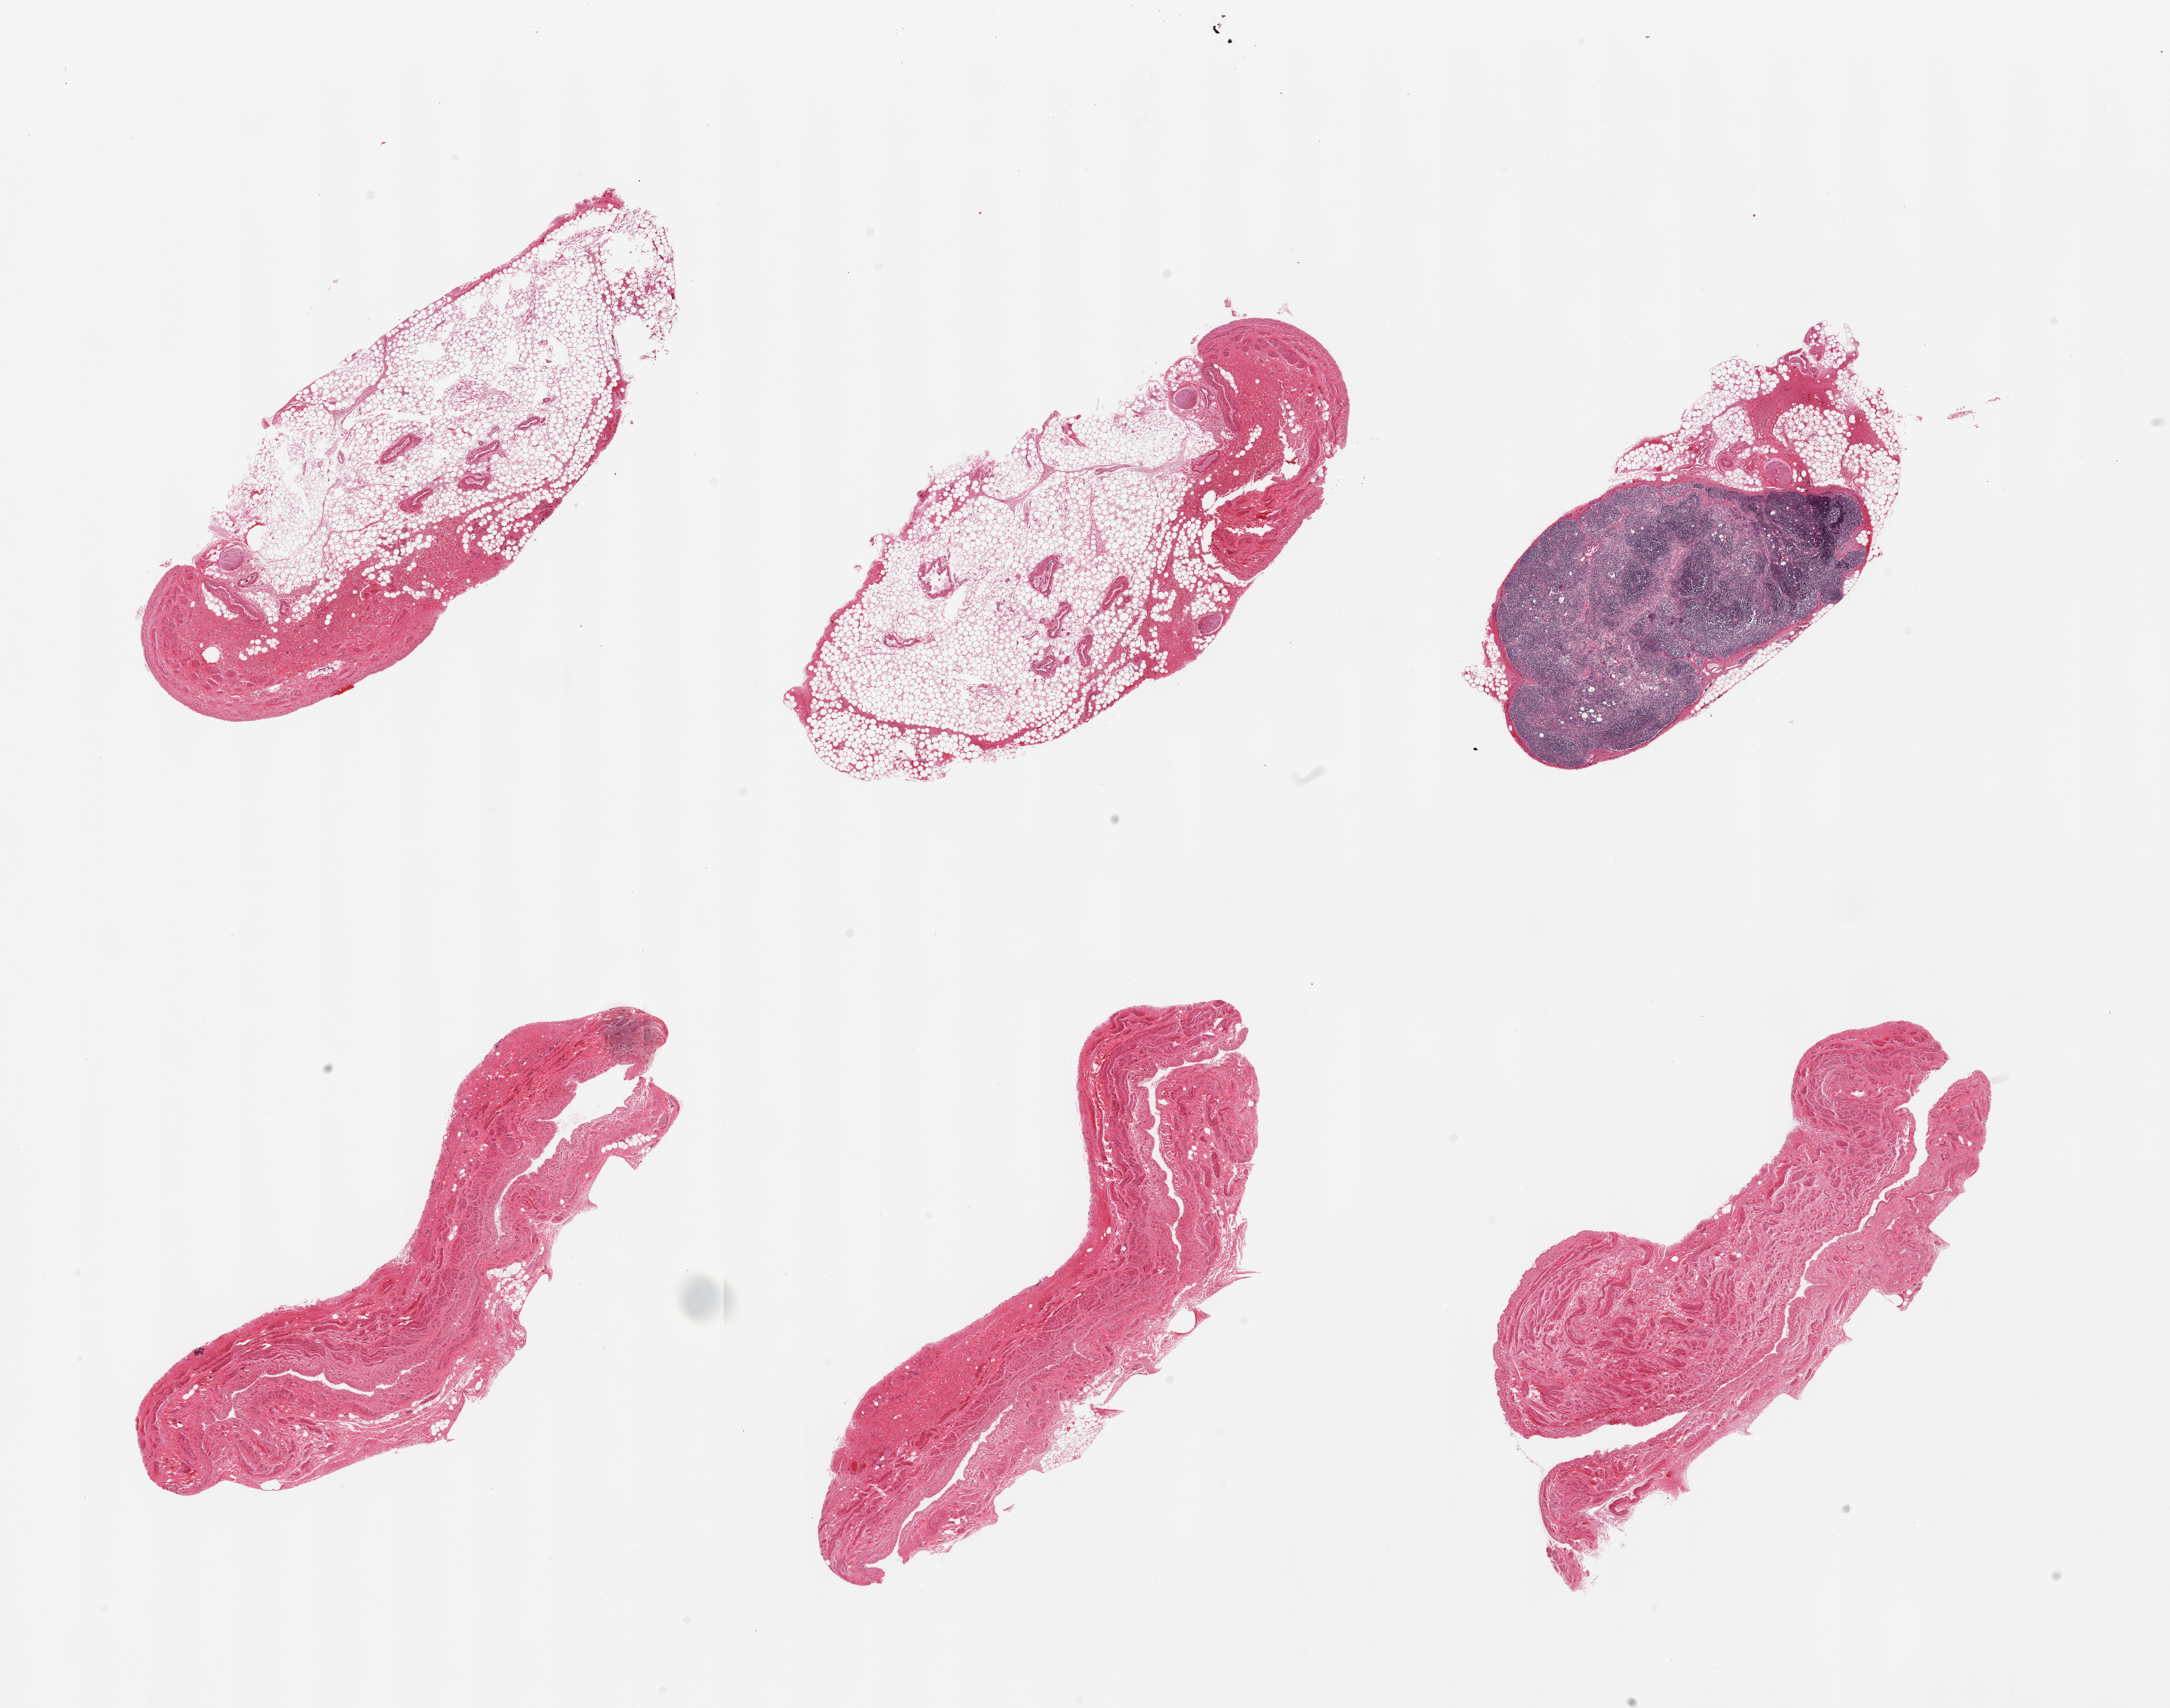
Digitized haematoxylin and eosin-stained section, brightfield — whole scanned area (about 26.6 x 20.9 mm, acquisition: 20x scan) shown as a low-resolution overview, PAXgene-fixed paraffin-embedded (PFPE) section, section of gastroesophageal junction (target tissue), donor tissue sample. Donor: male.
- review note (as recorded): 6 pieces; 2 are predominantly fat; 1 is lymph node with attached fat